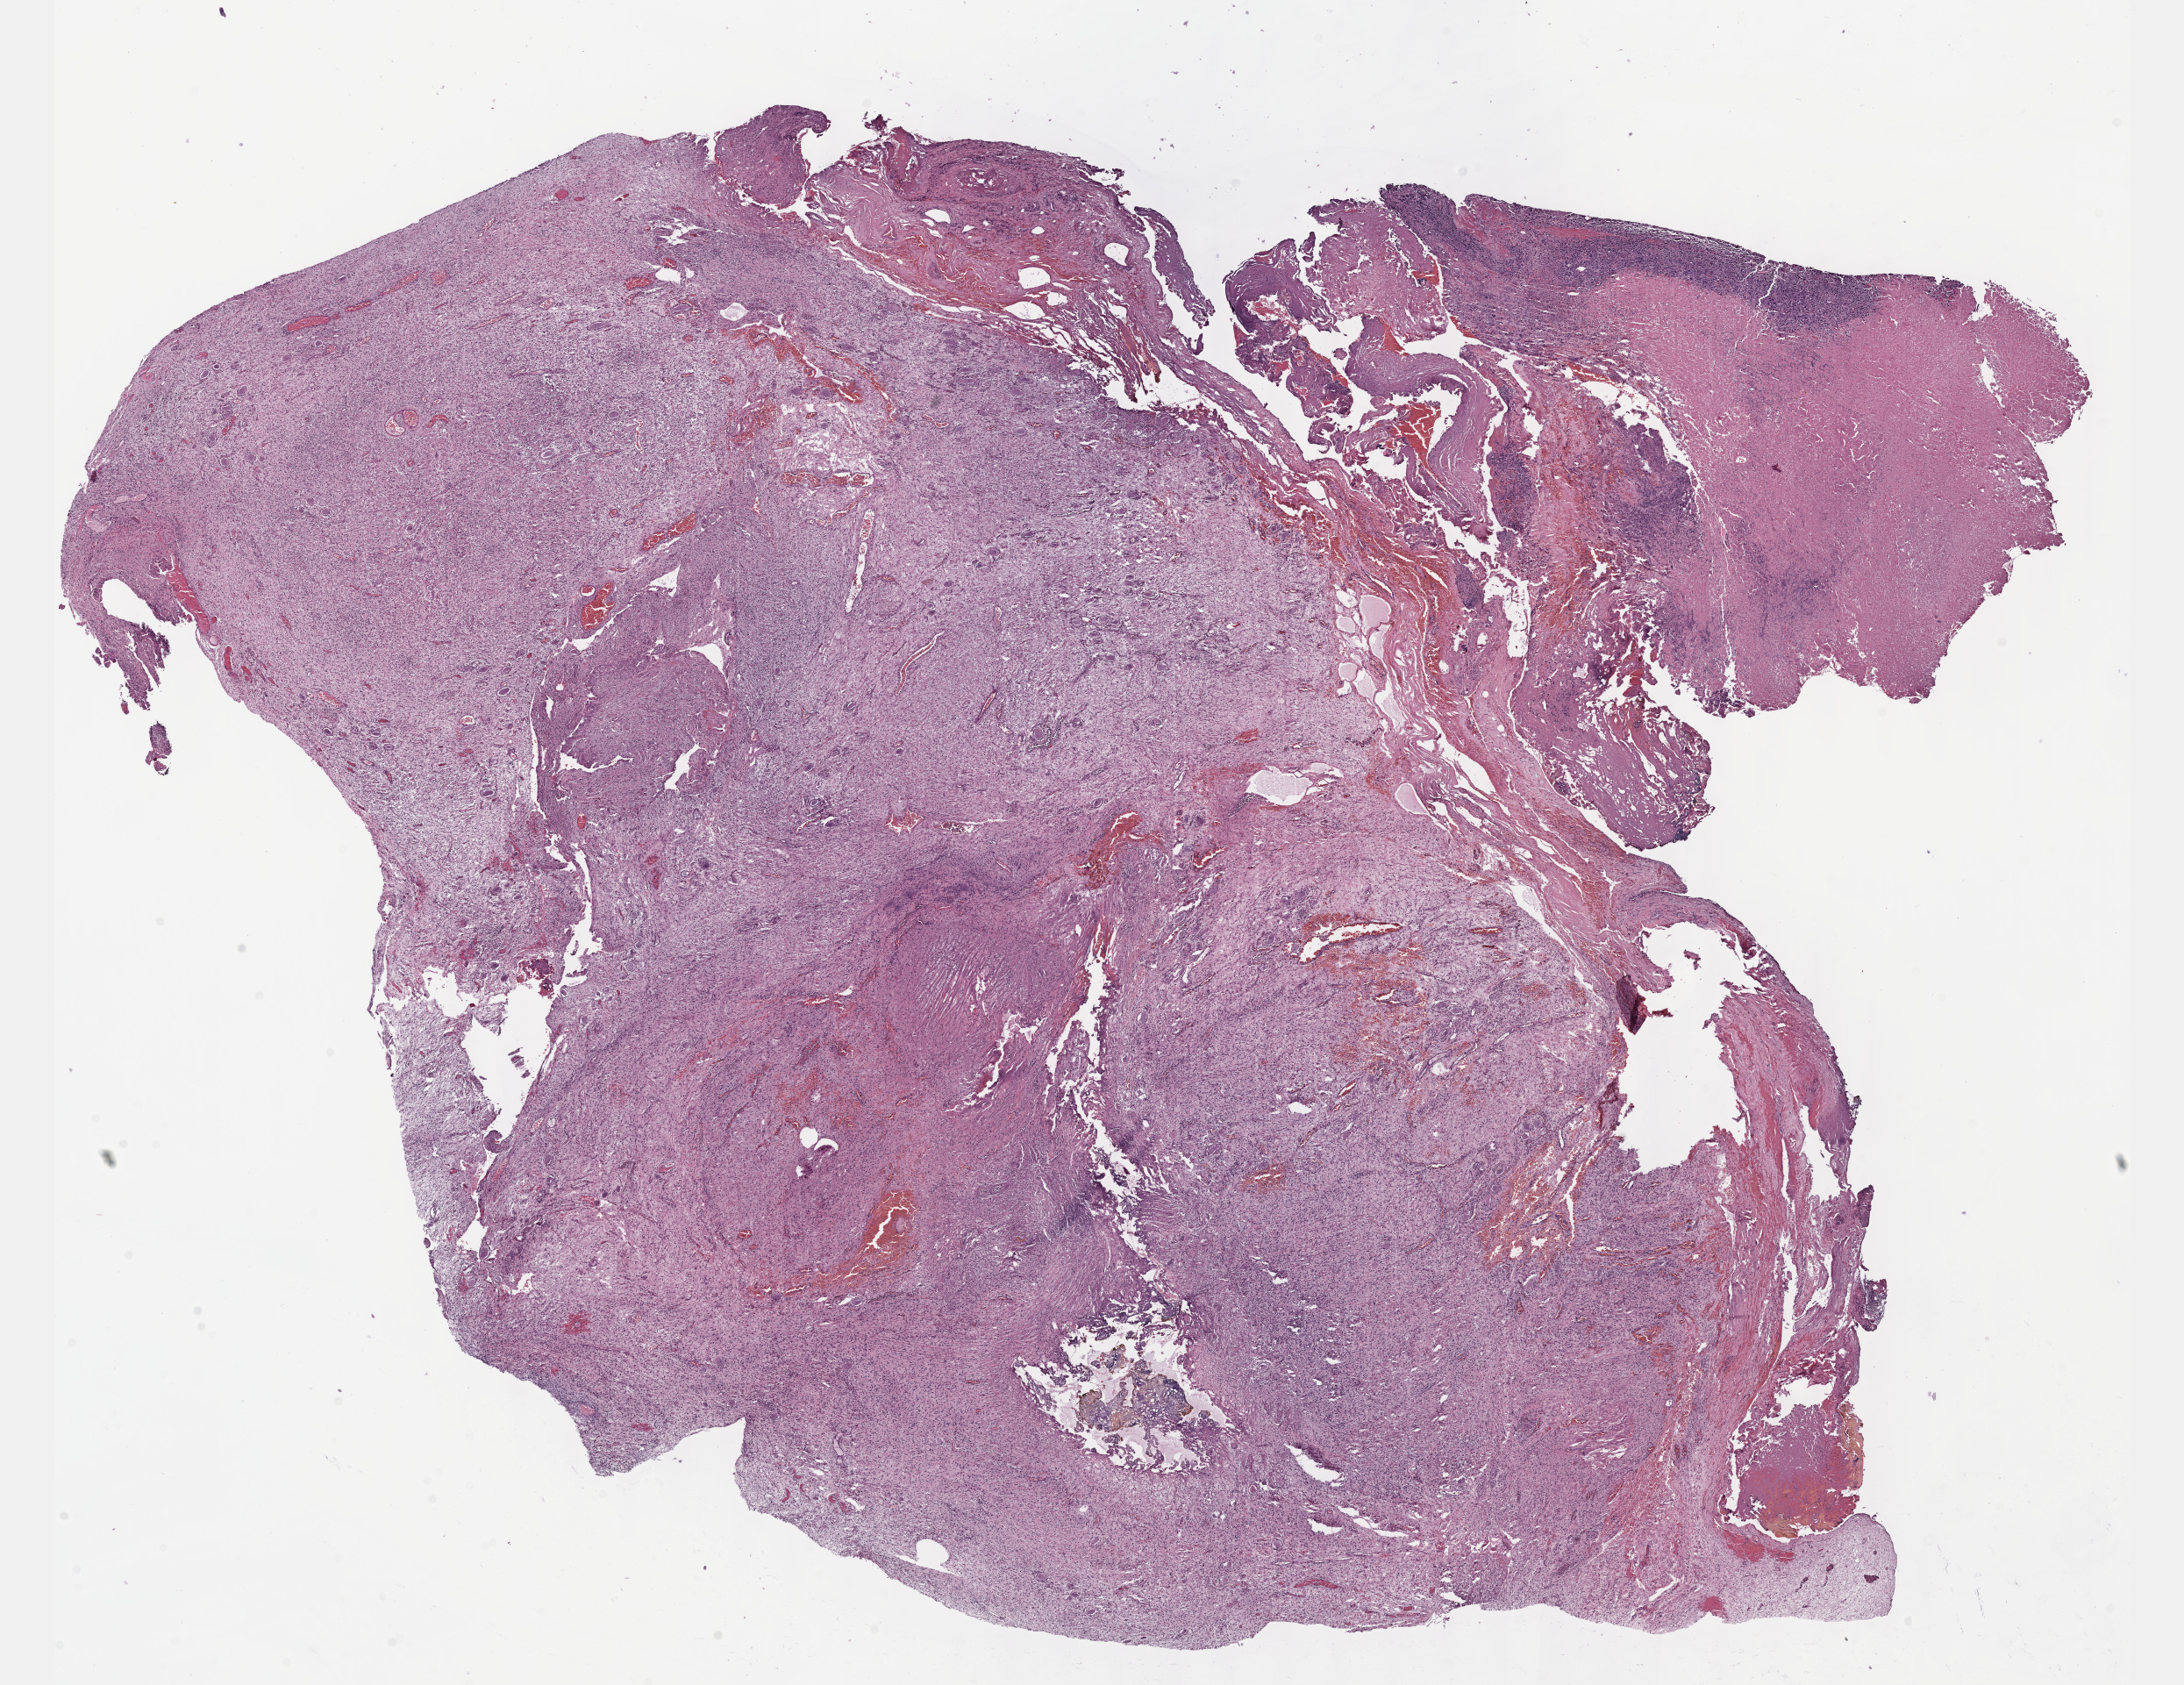
Digitized Hematoxylin and eosin (H&E) stained tissue section (whole slide) — low-resolution overview of the scanned area, about 20.1 x 15.5 mm, formalin-fixed paraffin-embedded (FFPE) diagnostic section, sample: primary tumour, peripheral nerves and autonomic nervous system. Patient: male, age at initial diagnosis 50 years.
* diagnosis: Malignant peripheral nerve sheath tumor (peripheral nerves and autonomic nervous system of upper limb and shoulder)